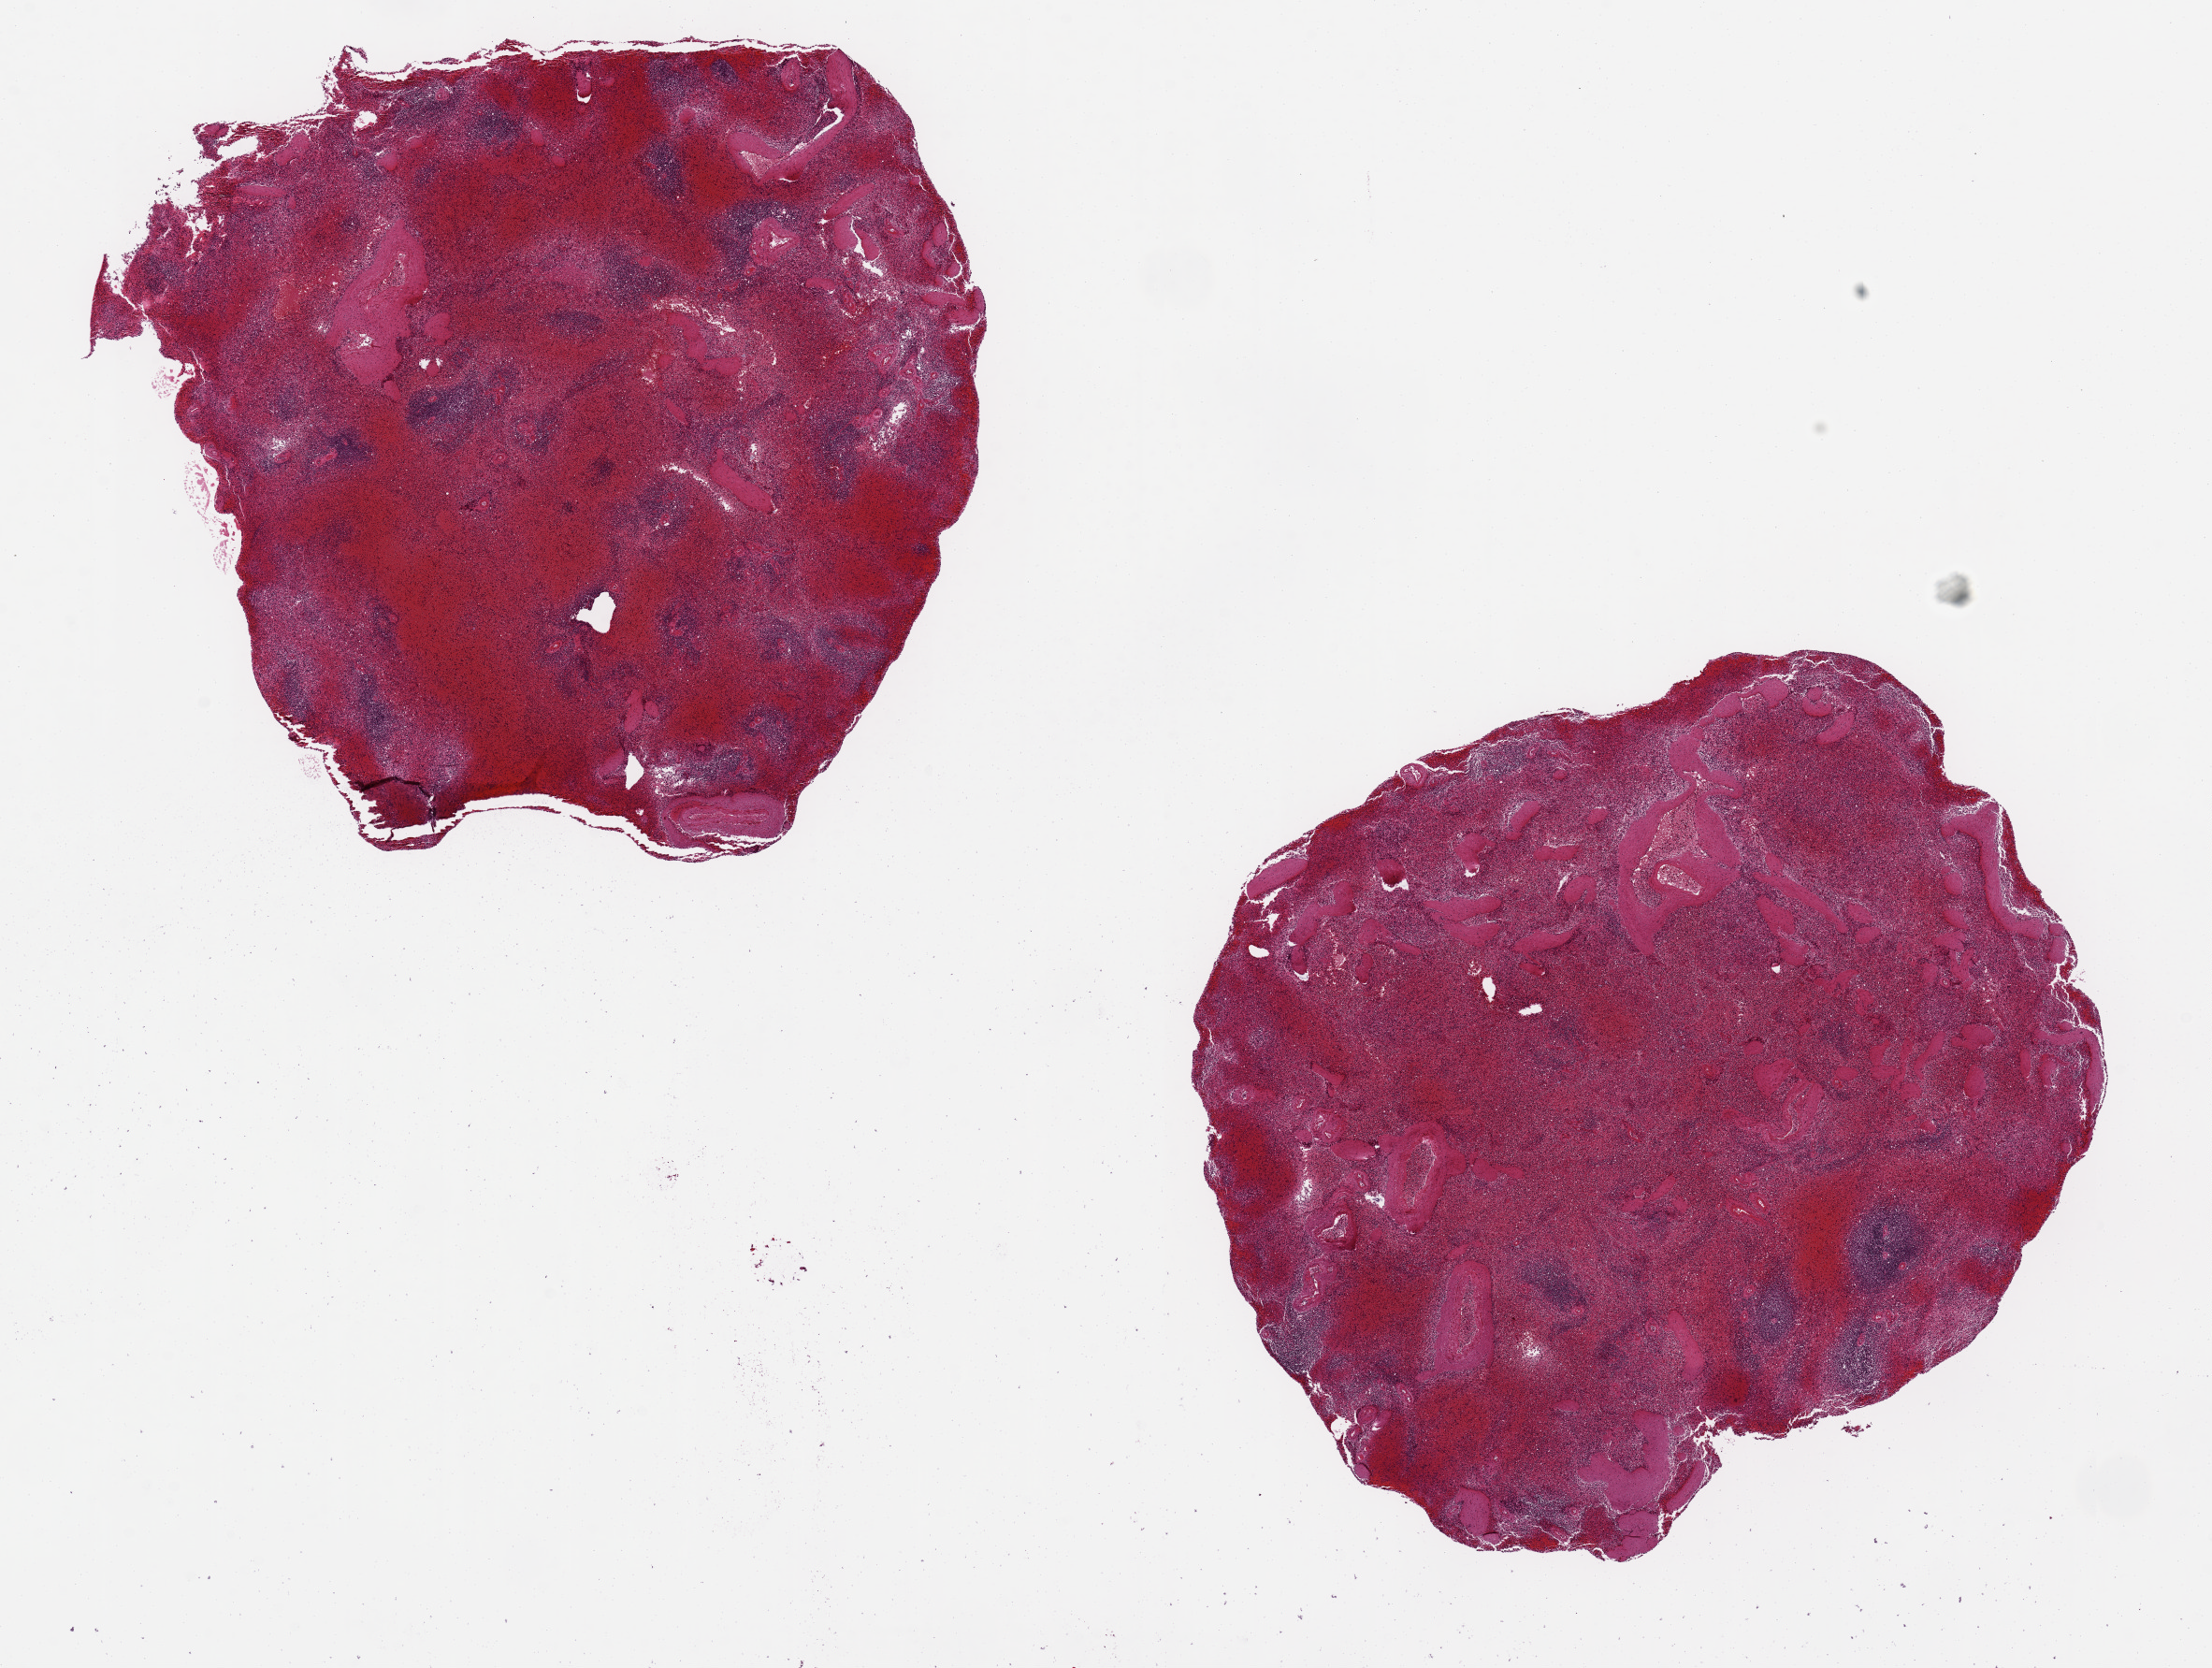
Haematoxylin and eosin whole-slide image, brightfield — whole scanned area (about 18.7 x 14.1 mm, slide scanned at 20x) shown as a low-resolution overview. PAXgene-fixed paraffin-embedded (PFPE) section. Sampled site (target tissue): spleen. Donor tissue sample. Donor sex: male.
Pathologist's review note for this sample: 2 aliquots, 7x7mm. Badly congested/autolyzed.